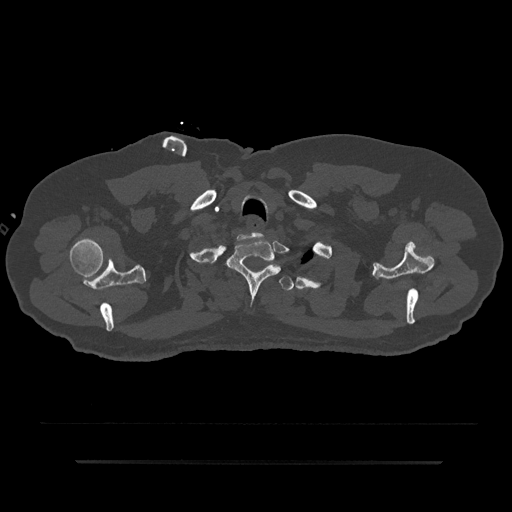
CT including the spine, one axial slice; reconstruction kernel Br40s/3; 120 kVp; bone window (W 1800 / L 400 HU); 0.5 mm slice thickness; 512 × 512 image matrix, field of view 464 × 464 mm. Patient: male, 59 years. Case-level facts recorded for this patient, not image findings: primary cancer: bile ducts; vertebrae with lytic lesions (as recorded): T10.
Outlined on this slice (semi-automatic segmentation, software-assisted and operator-edited):
- T1 vertebra: bounding box [x1, y1, x2, y2] px = [226, 237, 281, 298]
- T2 vertebra: [221, 264, 293, 291]